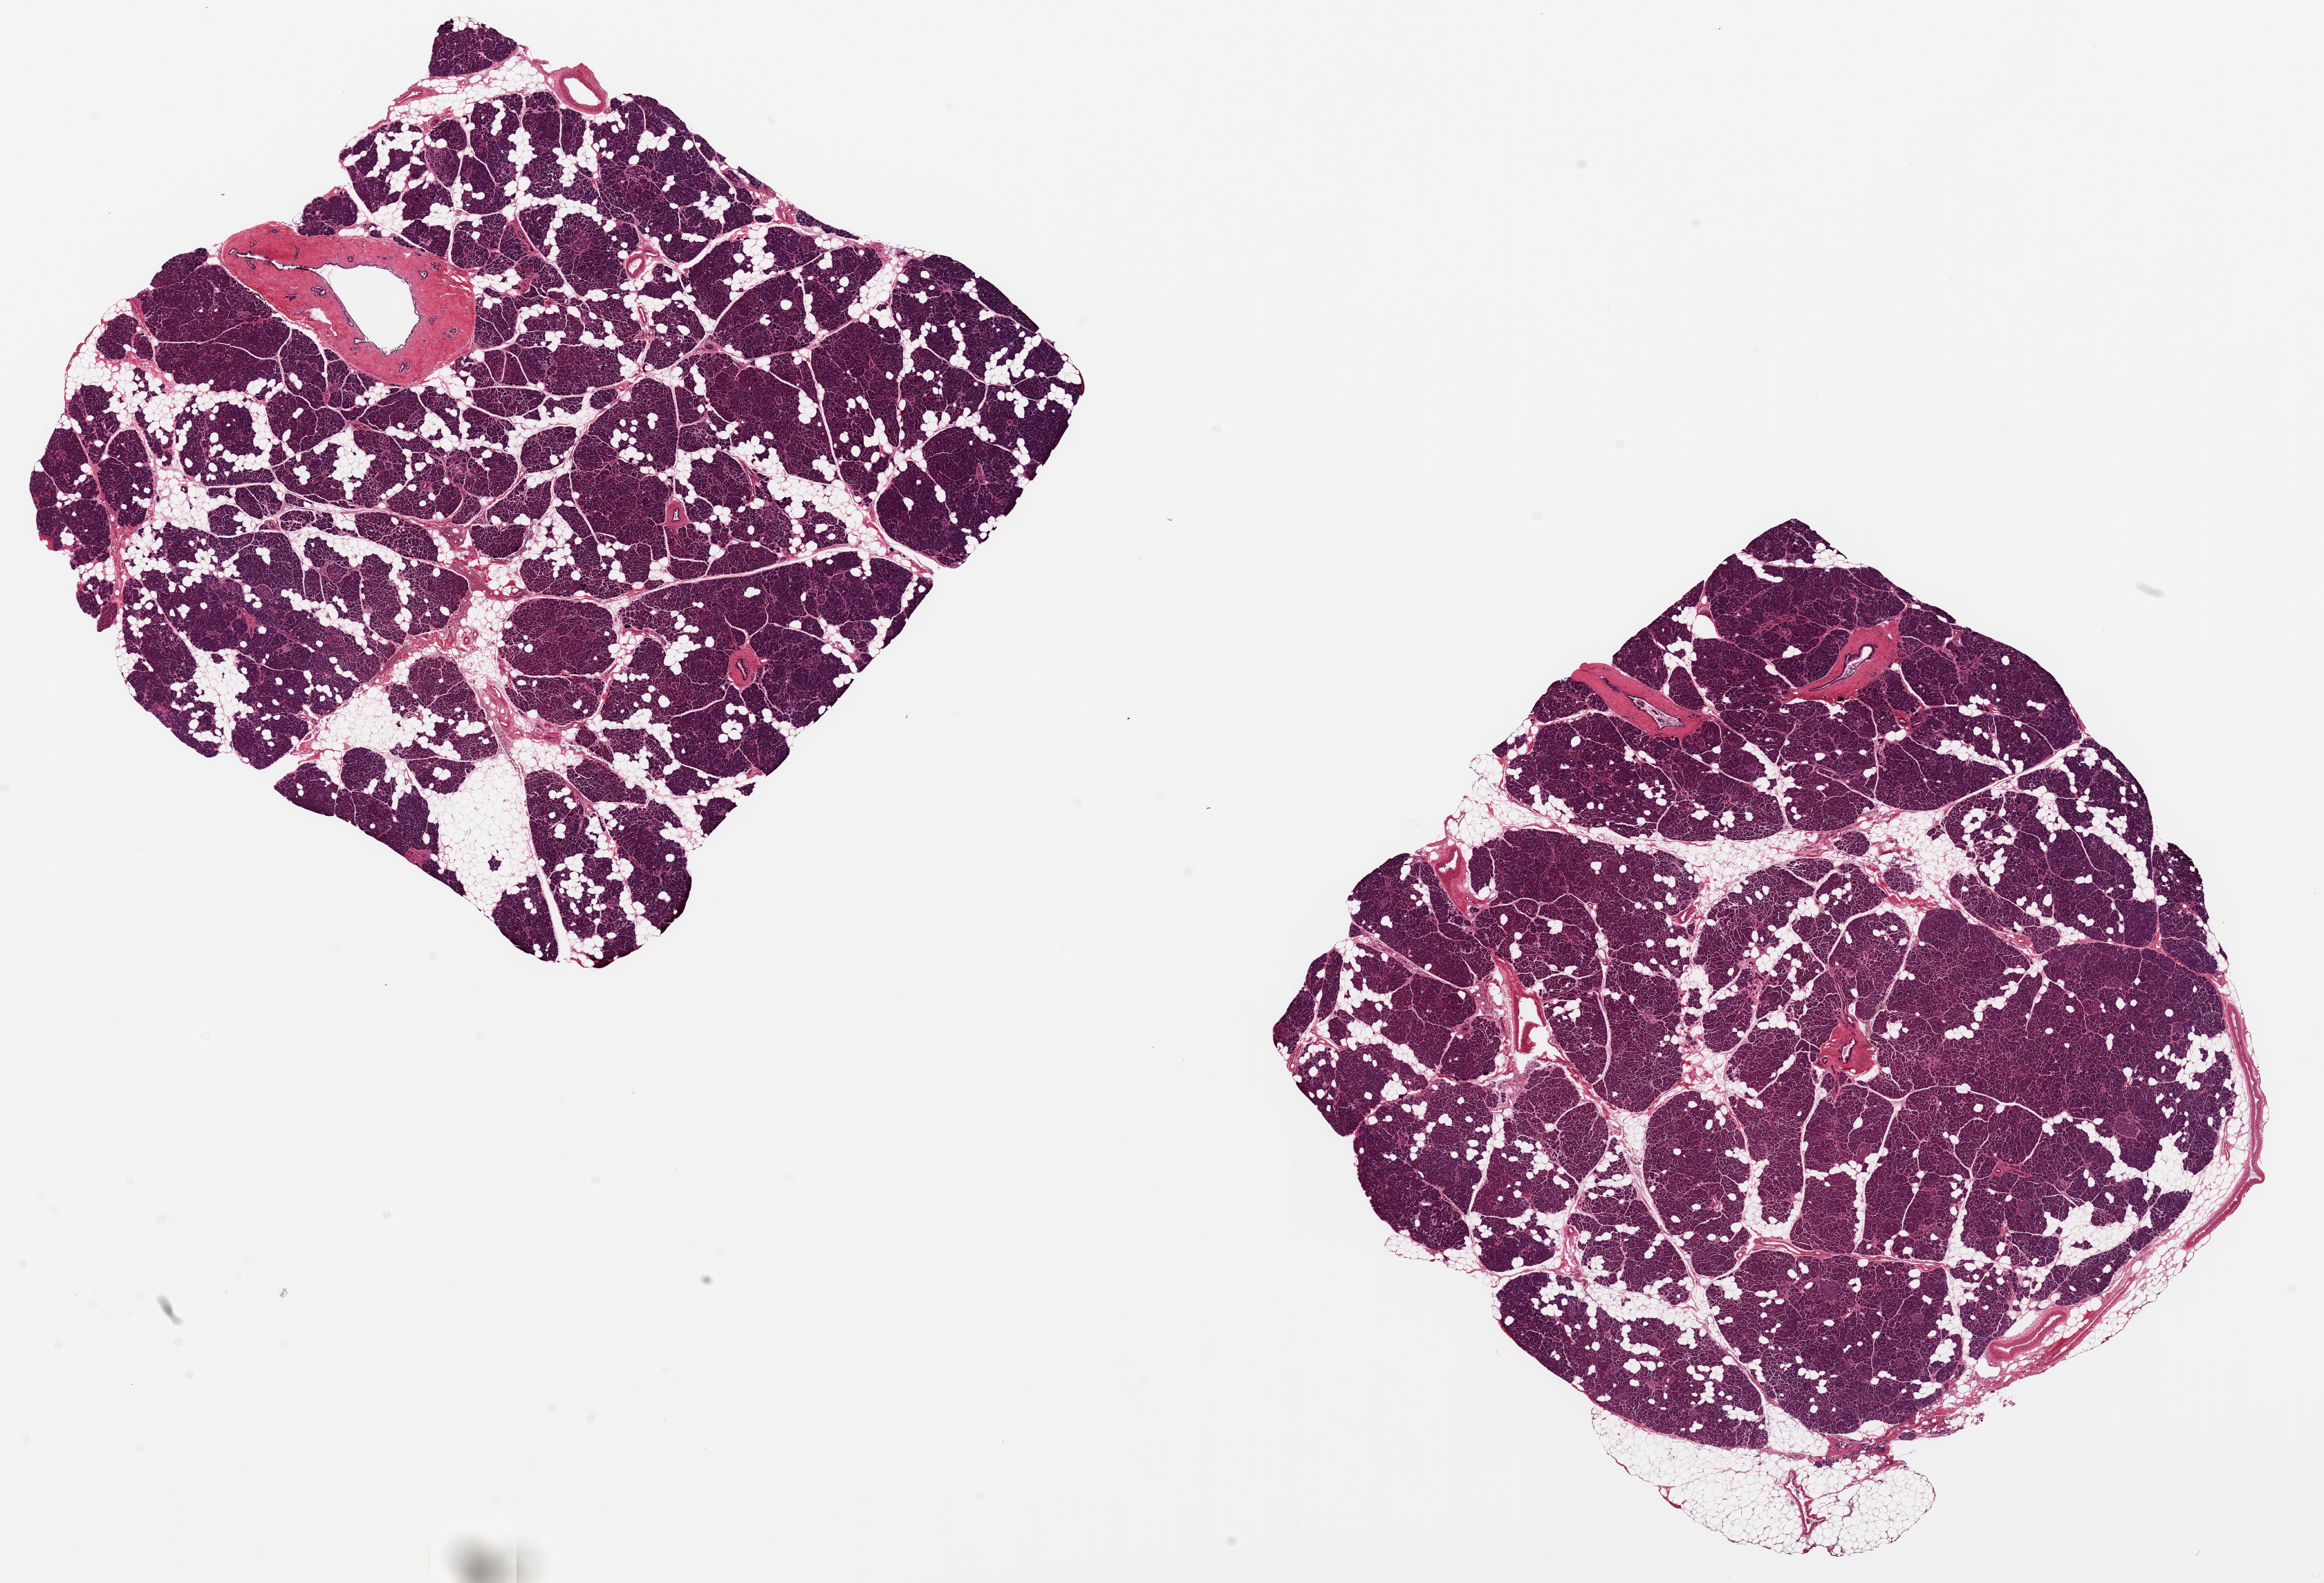
Whole-slide image, haematoxylin and eosin stain, brightfield — shown as a low-resolution overview of the whole scanned area (about 26.6 x 18.1 mm, slide scanned at 20x), PAXgene-fixed, paraffin-embedded tissue, target tissue: pancreas, tissue donor sample. Donor sex: male.
Review note (as recorded): 2 ~9x9mm pieces; ~20-30% intermingled fat.